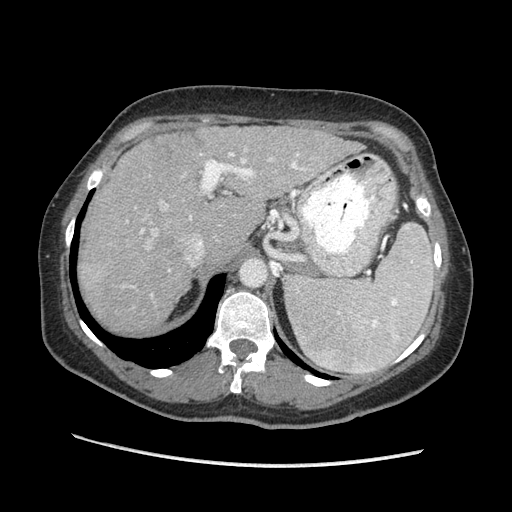
Contrast-enhanced abdominal CT (liver protocol), one axial slice. Position 140 of 170 along the scan axis. Reconstruction kernel STANDARD. 140 kVp. Soft-tissue window (W 400 / L 40 HU). 2.5 mm slice thickness. 512 × 512 image matrix, field of view 360 × 360 mm. From the clinical record (not read from this slice): diagnosis: hepatocellular carcinoma (patient treated with transarterial chemoembolisation; whether this scan precedes or follows treatment is not stated here); TNM stage (as recorded): Stage-II; Child-Pugh class: A; tumour differentiation: no biopsy; tumour nodularity: multinodular.
Annotated regions visible in this slice (semi-automatically segmented with operator editing):
- abdominal aorta: bounding box (x1, y1, x2, y2) in pixels: (241, 261, 266, 285)
- liver parenchyma outside the tumour (the mass and vessels are separate outlines, so this box may not span the whole liver): (80, 126, 362, 332)
- liver vessels: (140, 152, 307, 296)